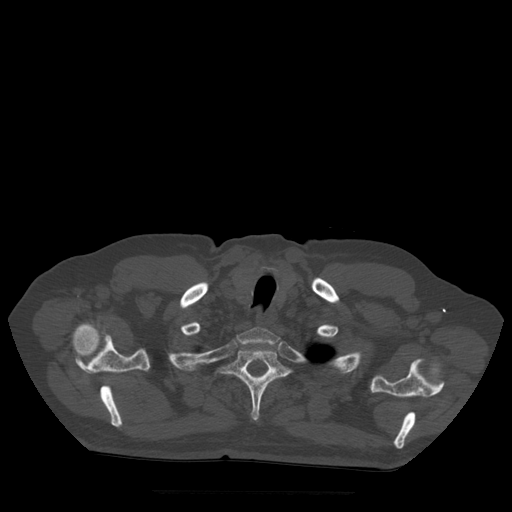
CT including the spine, one axial slice. Position 427 of 522 along the scan axis. Bone window (W 1800 / L 400 HU). 1.25 mm slice thickness. 512 × 512 image matrix, field of view 420 × 420 mm. Patient age 72 years. From the clinical record (not read from this slice): primary cancer: prostate.
Annotated regions visible in this slice (semi-automatically segmented with operator editing):
- T1 vertebra: box from (x=237, y=328) to (x=280, y=345) px
- T2 vertebra: (x=219, y=348)–(x=291, y=421)